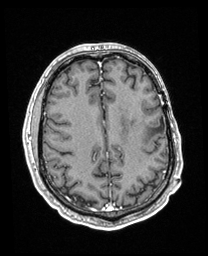
Brain MRI from a brain-tumour surgery series, one axial slice. Position 79 of 208 along the scan axis. T1-weighted post-contrast. 1 mm slice thickness. 208 × 256 image matrix. Case-level facts recorded for this patient, not image findings: histopathology: Astrocytoma; WHO grade: 3; IDH mutation: yes; tumour location: Left Insular.
Structures marked on this image (outlined manually by an expert reader):
- previous resection cavity: bounding box (x1, y1, x2, y2) in pixels: (155, 117, 164, 132)